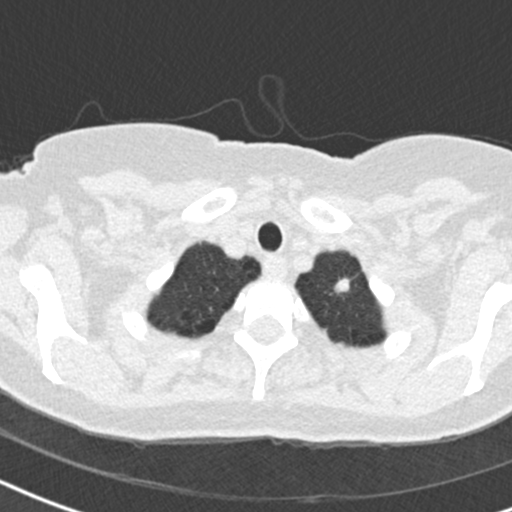
Low-dose screening chest CT, one axial slice; position 171 of 184 along the scan axis; reconstruction kernel B30f; 120 kVp; lung window (W 1500 / L -600 HU); 512 × 512 image matrix, field of view 280 × 280 mm.
Structures marked on this image (manually delineated by an expert):
- lesion 1 (tumor, upper lobe of left lung): bounding box (x1, y1, x2, y2) in pixels: (334, 278, 350, 293)